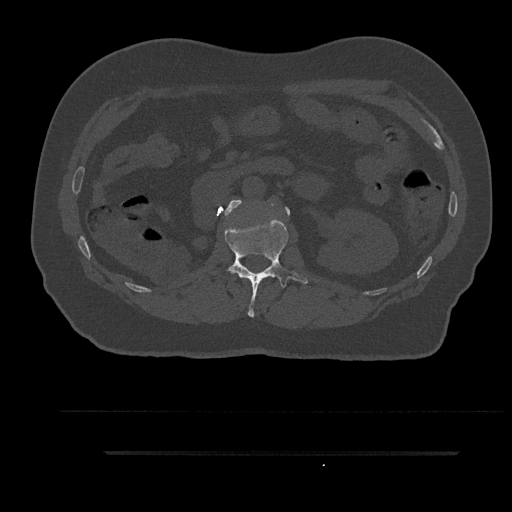
CT including the spine, one axial slice. Slice 165 of 797 in the series (ordered by position). Bone window (W 1800 / L 400 HU). 0.5 mm slice thickness. 512 × 512 image matrix. Patient: male, 63 years. Case-level facts recorded for this patient, not image findings: primary cancer: renal.
Outlined on this slice (semi-automatic segmentation, software-assisted and operator-edited):
- L1 vertebra: bounding box <225,218,308,318> (left, top, right, bottom; pixels)
- L2 vertebra: <224,200,290,216>